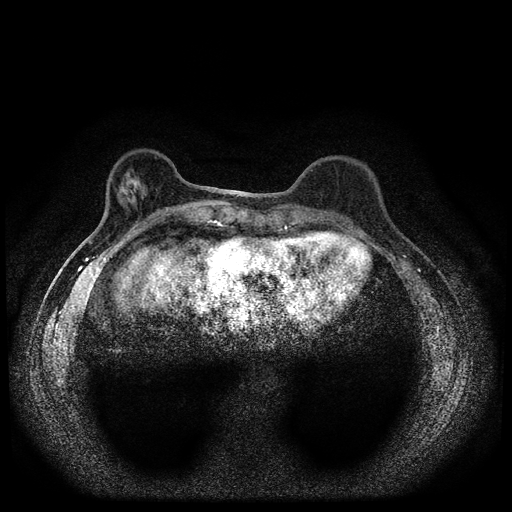
Breast MRI (dynamic contrast-enhanced, multi-phase), one axial slice; slice 29 of 112 in the series (ordered by position); dynamic contrast-enhanced series, time point 2 of 5 at this slice position (early post-contrast); 1.5 T; TE 2.7 ms, TR 5.4 ms; 2 mm slice thickness; 512 × 512 image matrix, field of view 320 × 320 mm. Patient: female, 61 years.
Outlined on this slice (semi-automatic segmentation, software-assisted and operator-edited):
- breast lesion (labelled benign in the annotation): box from (x=119, y=169) to (x=141, y=205) px